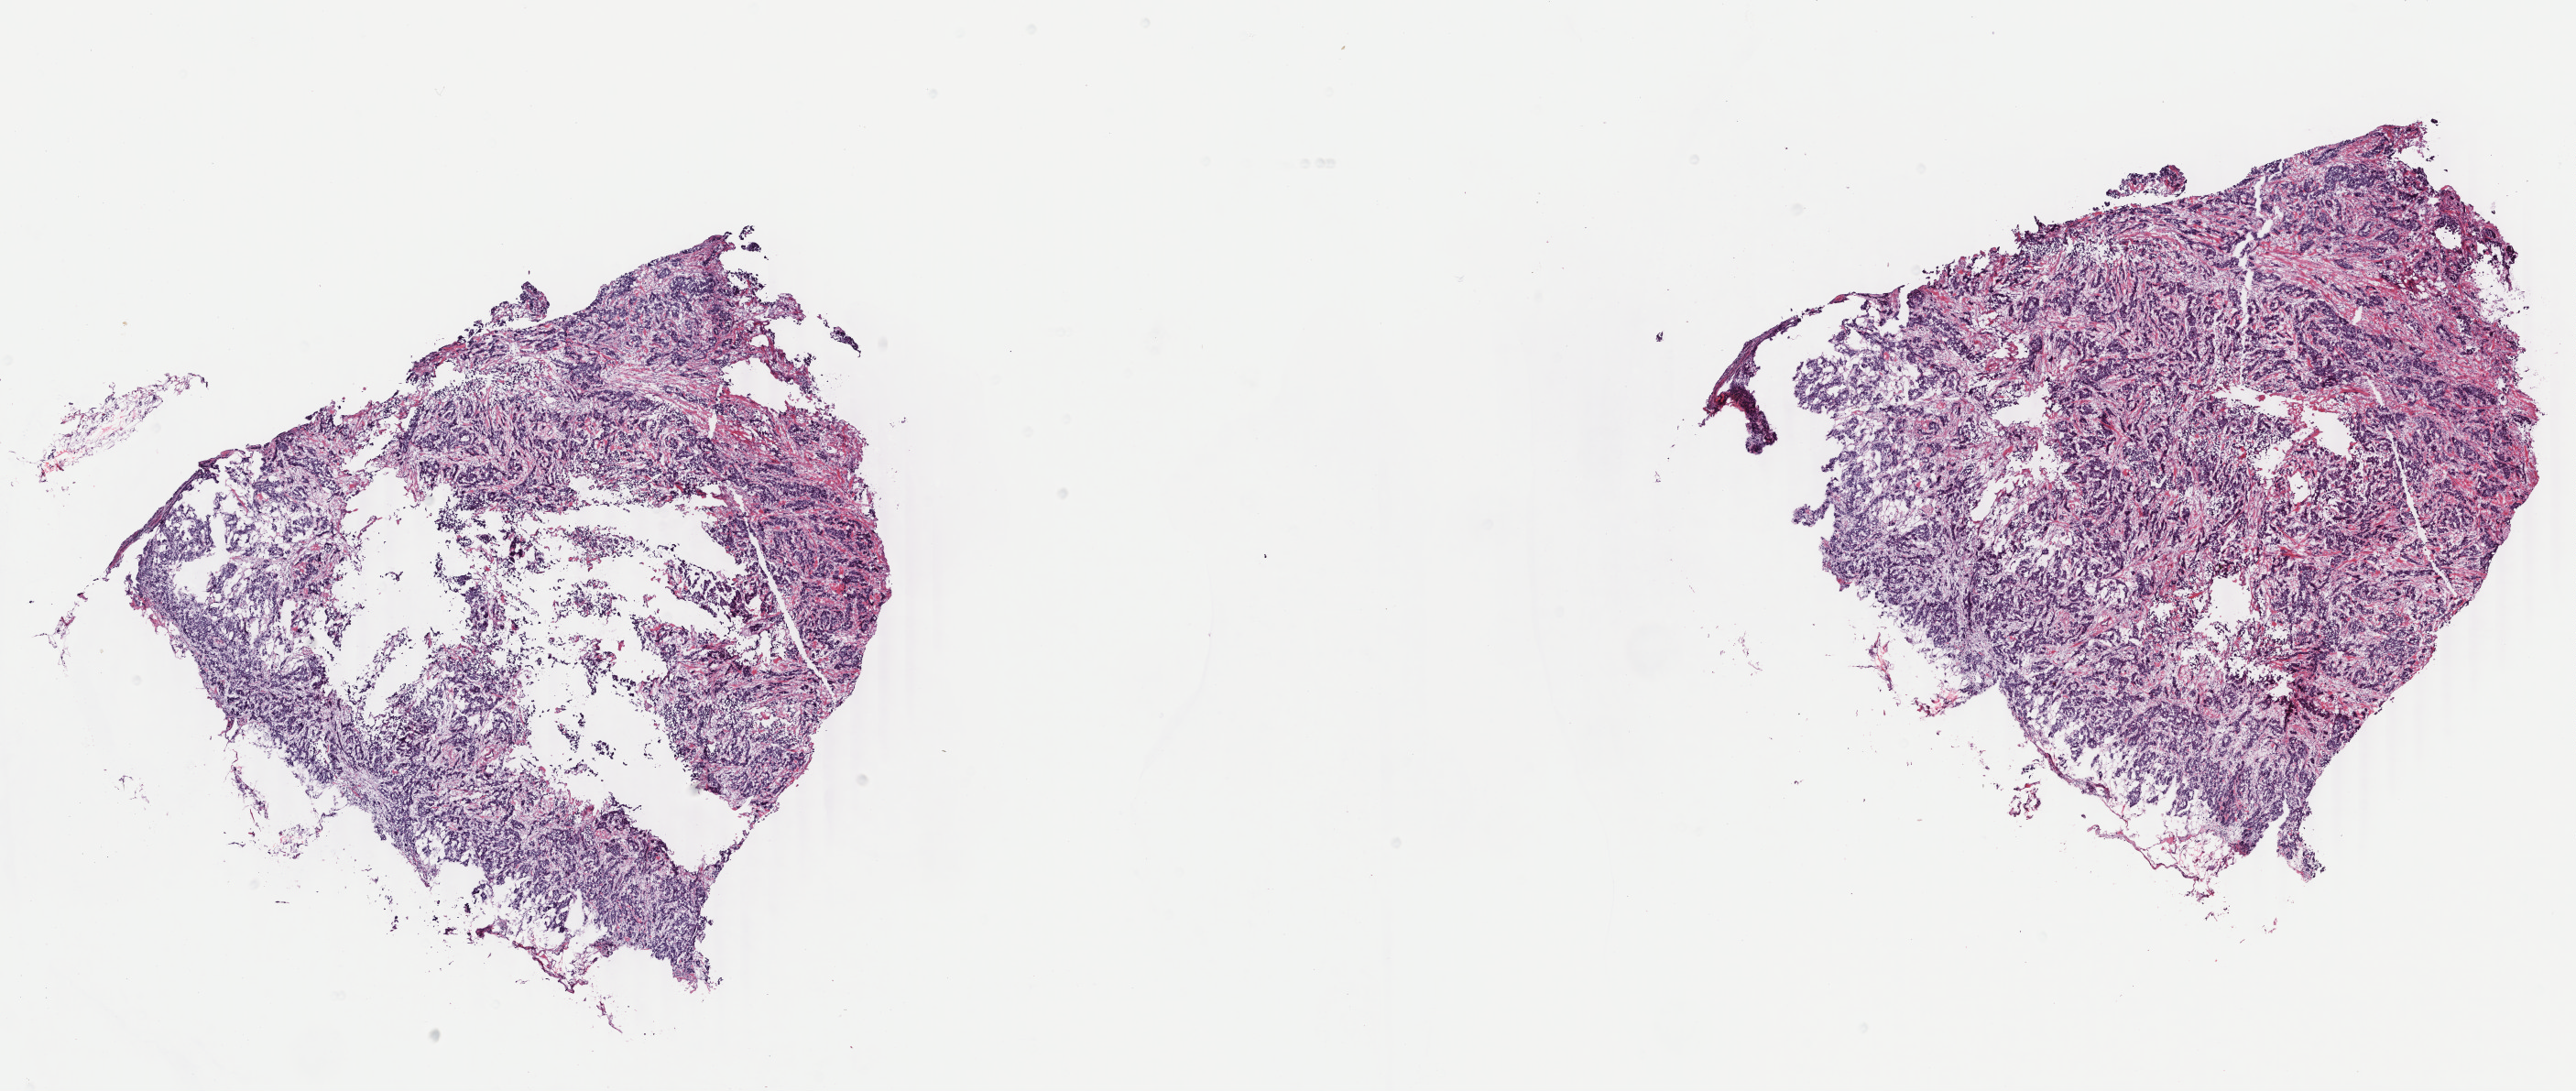
Digitized H&E-stained tissue section (whole slide), low-resolution overview of the scanned area, about 22.4 x 9.5 mm, frozen section, primary tumour sample from the breast. Patient: female, age at initial diagnosis 45 years. Composition of this section per pathologist review: tumour cells 100%, tumour nuclei 90%, normal cells 0%, stromal cells 0%, necrosis 0%. Inflammatory infiltration, as recorded: lymphocyte infiltration 0%, monocyte infiltration 0%, neutrophil infiltration 0%.
Laterality: left. Lymph nodes positive (case pathology): 1 of 14 examined. Histologic diagnosis: Infiltrating duct carcinoma, NOS. AJCC pathologic stage: IIIA.